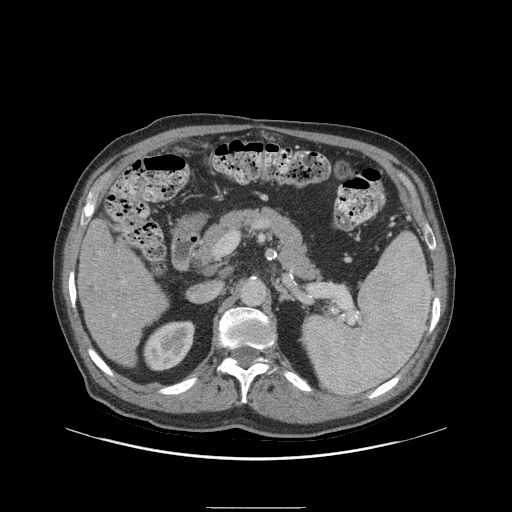
Contrast-enhanced abdominal CT (liver protocol), one axial slice; 140 kVp; soft-tissue window (W 400 / L 40 HU); 512 × 512 image matrix. Case-level facts recorded for this patient, not image findings: diagnosis: hepatocellular carcinoma (patient treated with transarterial chemoembolisation; whether this scan precedes or follows treatment is not stated here); TNM stage (as recorded): Stage-I; Child-Pugh class: A; tumour nodularity: uninodular; tumour size: 5.1 cm.
Structures marked on this image (semi-automatically segmented with operator editing):
- liver parenchyma outside the tumour (the mass and vessels are separate outlines, so this box may not span the whole liver): bounding box <78,218,167,366> (left, top, right, bottom; pixels)
- liver vessels: <113,314,116,317>